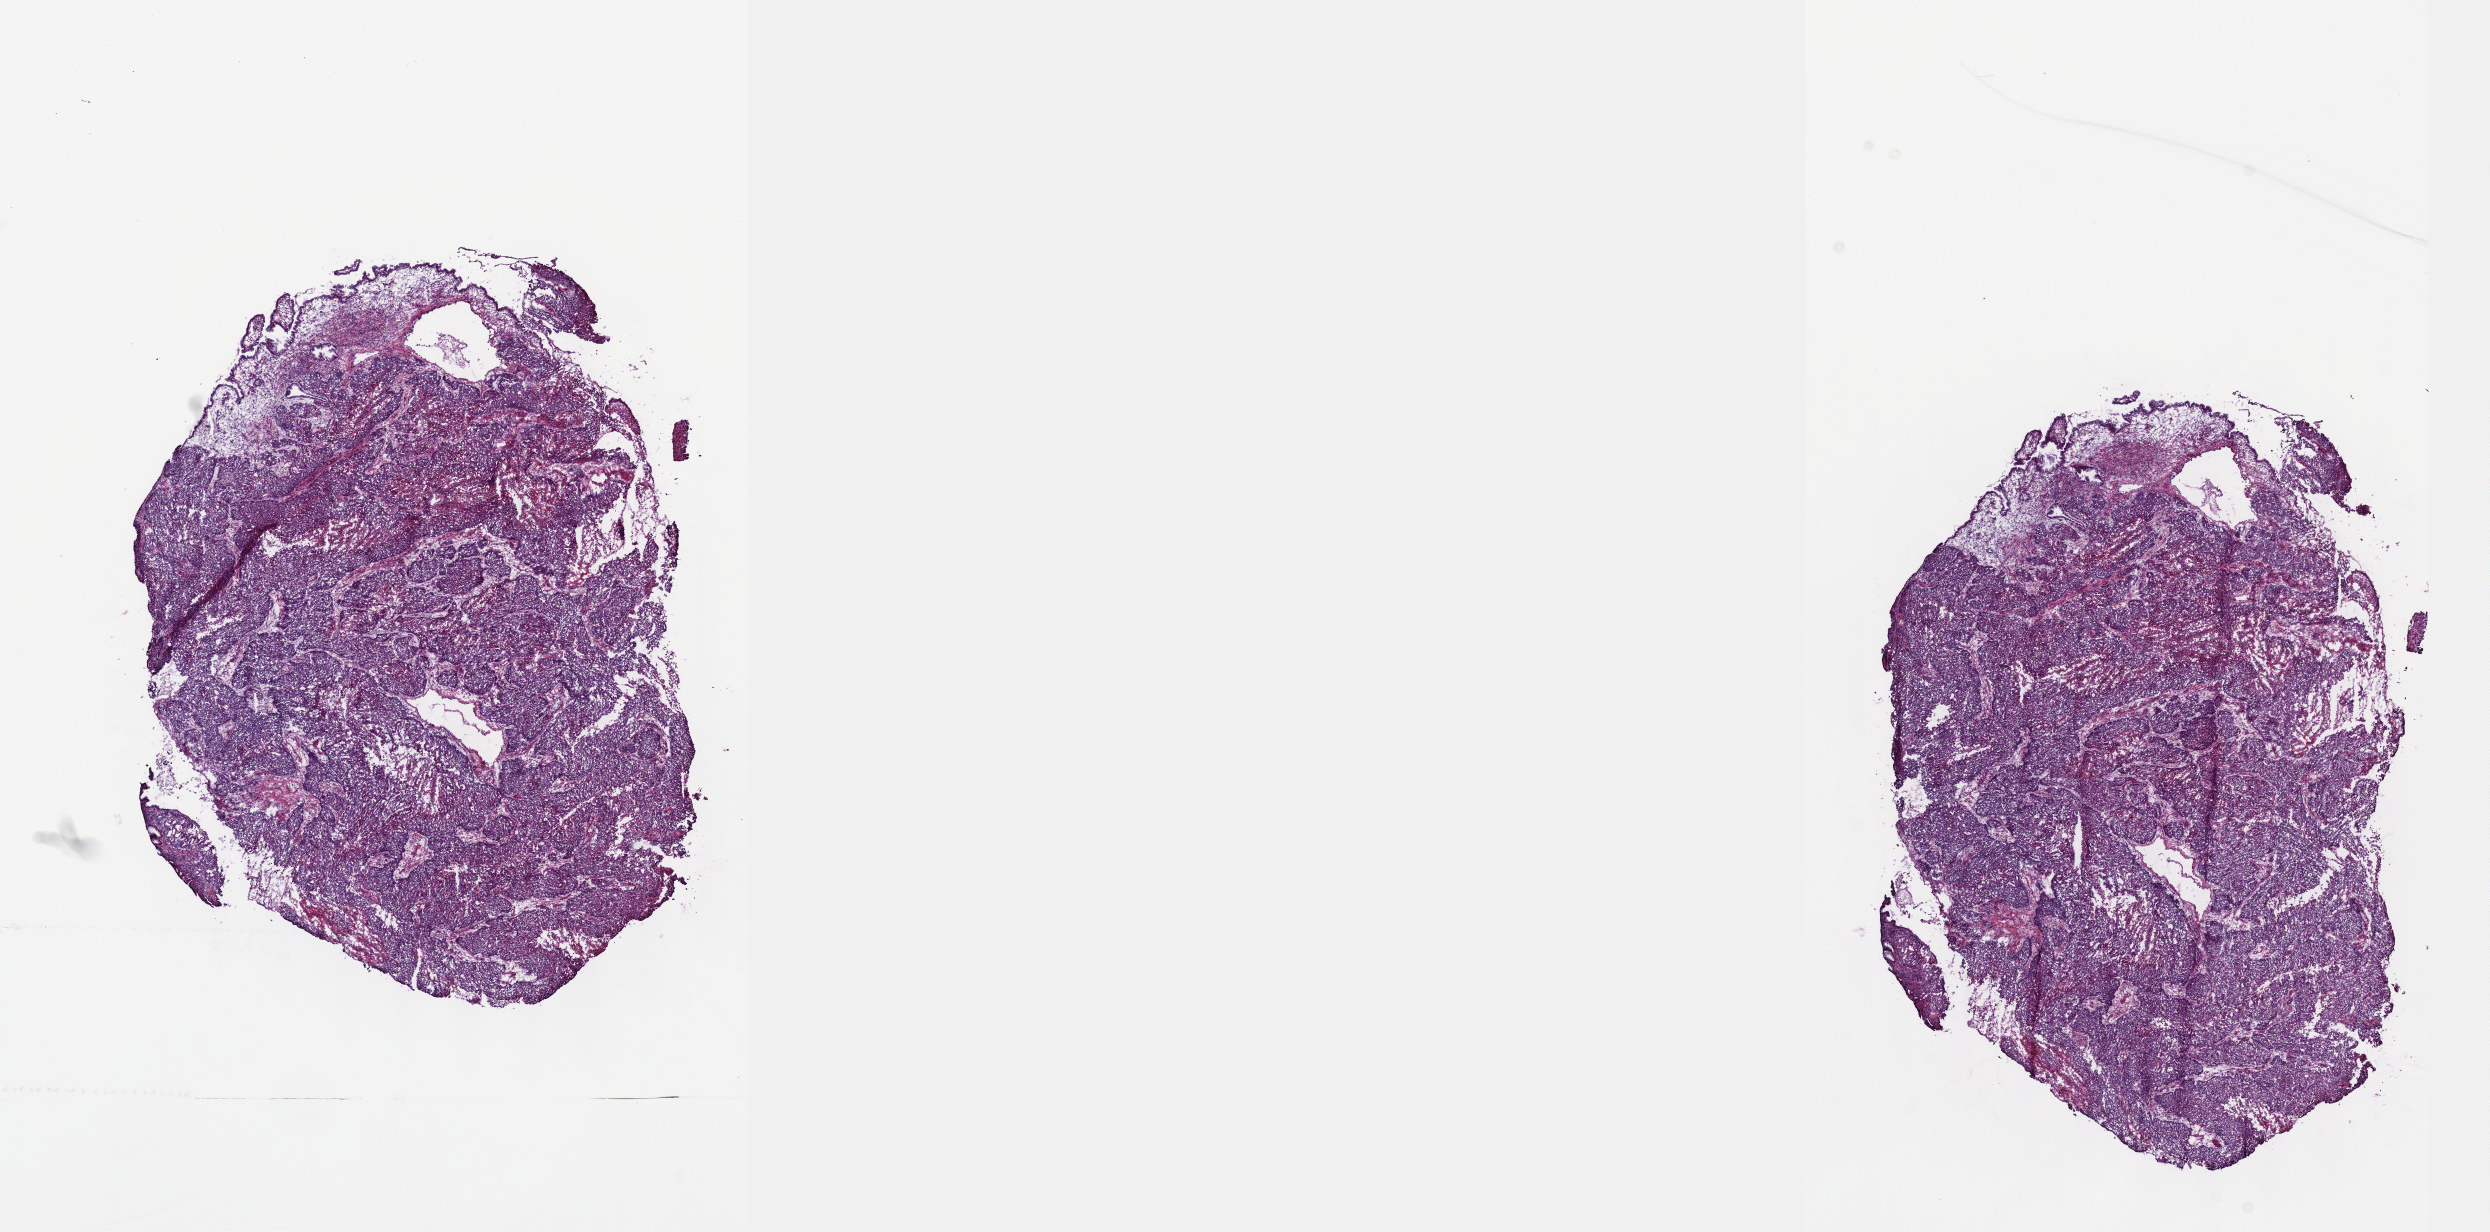
Whole-slide histology image, Hematoxylin and eosin (H&E) stained, shown as a low-resolution overview of the whole scanned area (about 20.1 x 10.0 mm, acquisition: 40x scan), frozen section from the top of the tissue portion, cervix, primary tumour sample. Female patient; age at initial diagnosis 55 years. Histologic grade: GX (grade cannot be assessed). Slide review estimates, as recorded: tumour cells 80%, tumour nuclei 80%, normal cells 5%, stromal cells 13%, necrosis 2%. Inflammatory infiltration, as recorded: lymphocyte infiltration 5%, monocyte infiltration 0%, neutrophil infiltration 5%.
Histologic diagnosis: Squamous cell carcinoma, NOS (cervix uteri). FIGO stage: IIB.